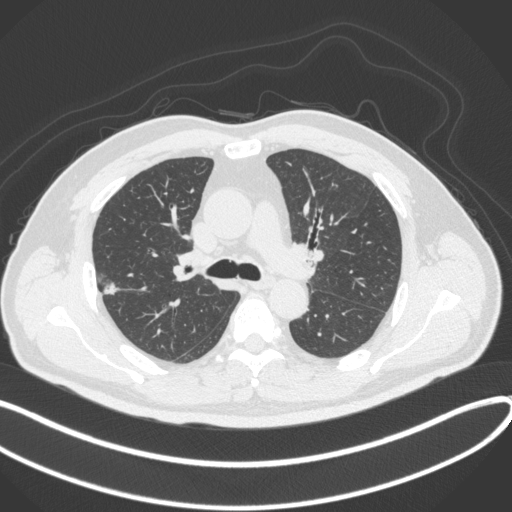
Chest CT, one axial slice. Slice 222 of 373 in the series (ordered by position). Lung window (W 1500 / L -600 HU). 512 × 512 image matrix, field of view 400 × 400 mm. Male patient, age 60 years. Case-level facts recorded for this patient, not image findings: clinical TNM (as recorded): T1c N0 M0.
Outlined on this slice (bounding box drawn by a radiologist):
- lung tumour (recorded histology: adenocarcinoma): bounding box [x1, y1, x2, y2] px = [94, 271, 124, 301]